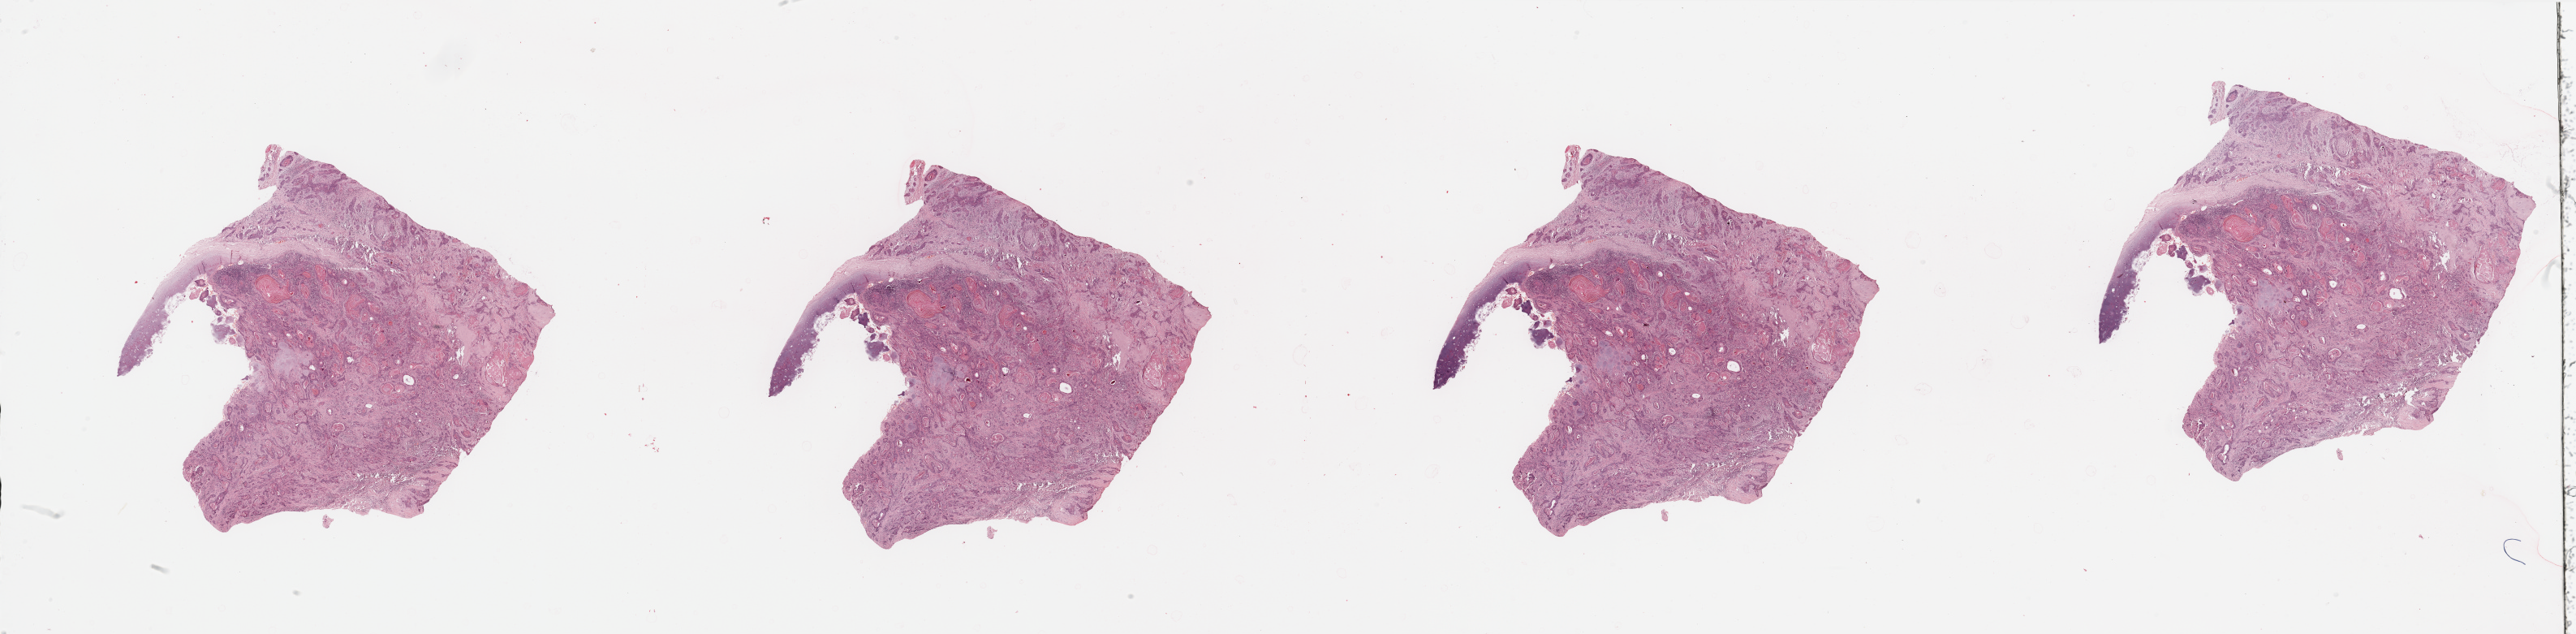
Digitized H&E-stained tissue section (whole slide), low-resolution overview of the scanned area, about 50.2 x 12.4 mm, tumour tissue sample, sampled site: larynx. 81-year-old male patient. Histologic grade: G2 (moderately differentiated). Composition of this section per pathologist review: tumour nuclei 80%, necrosis 5%.
• primary tumour site (as recorded): larynx
• AJCC pathologic stage: I
• histologic diagnosis: Squamous cell carcinoma, NOS (larynx, NOS)